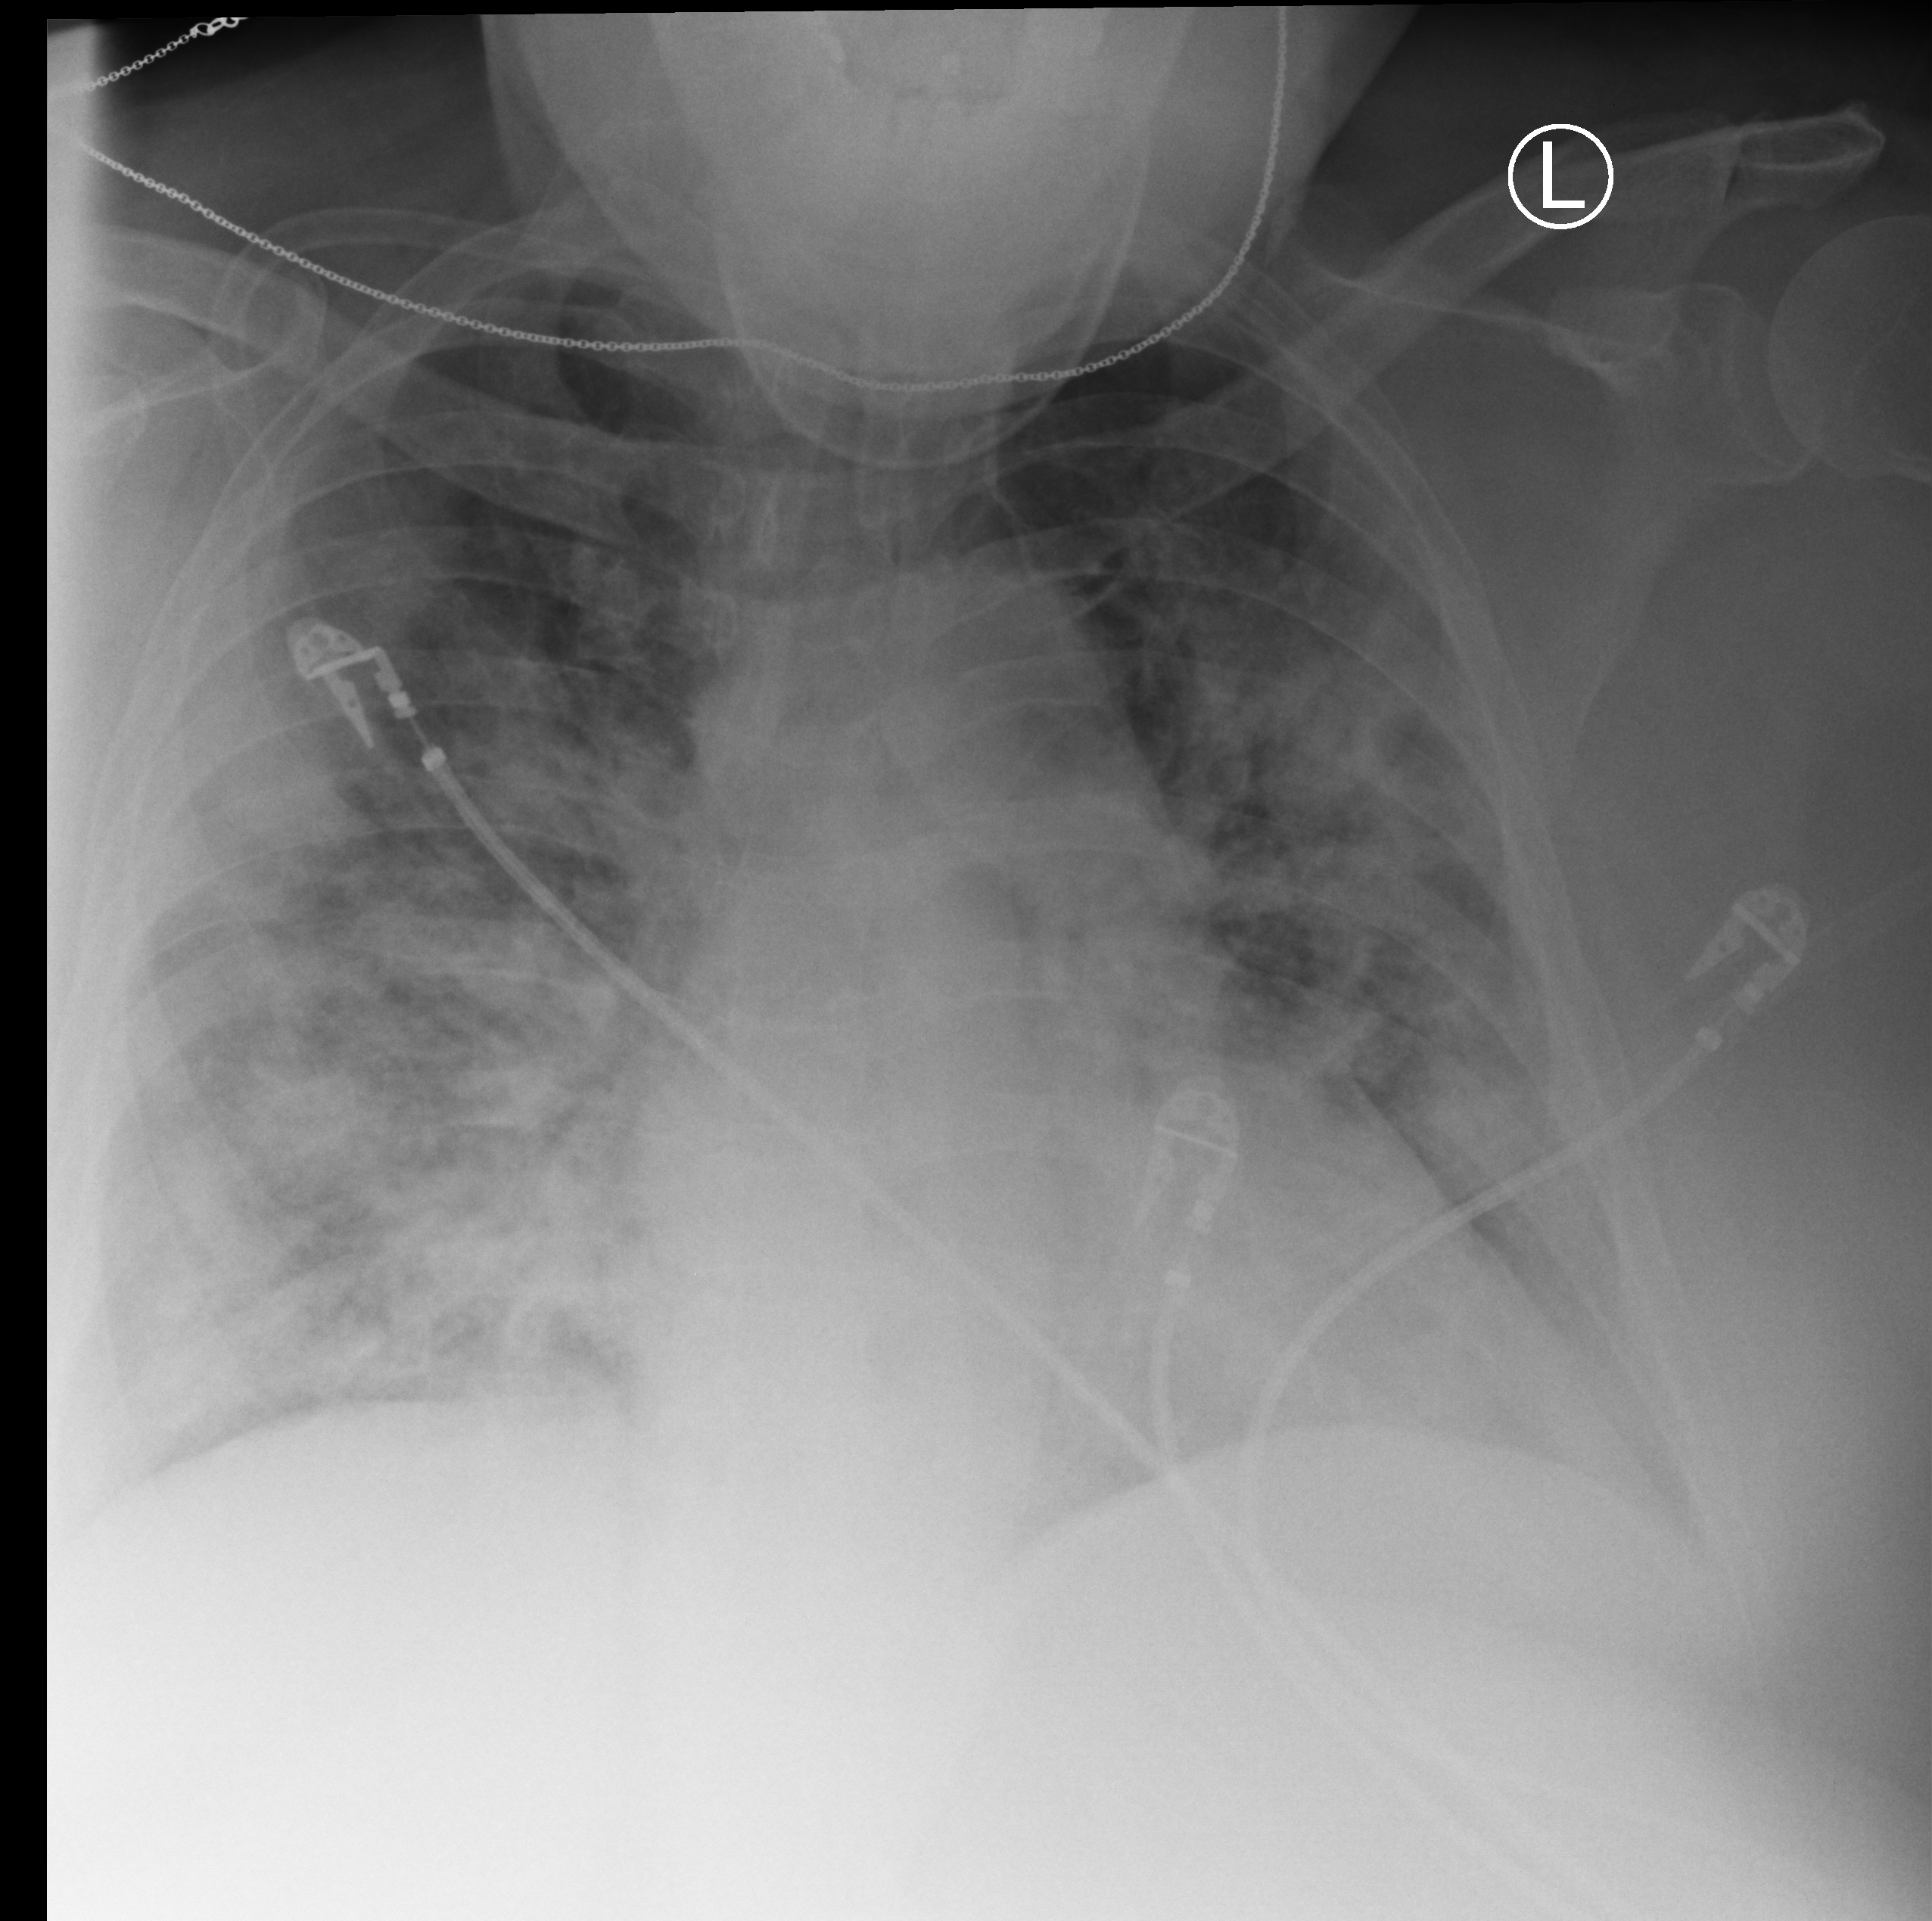
Portable chest radiograph. Female patient hospitalised with COVID-19, age 60–74 years.
Hospital-stay facts (about this admission, not read from this image; timing relative to this image not recorded): mechanically ventilated during this hospital stay: no; admitted to intensive care during this hospital stay: no; other chronic lung disease (admission record): no.